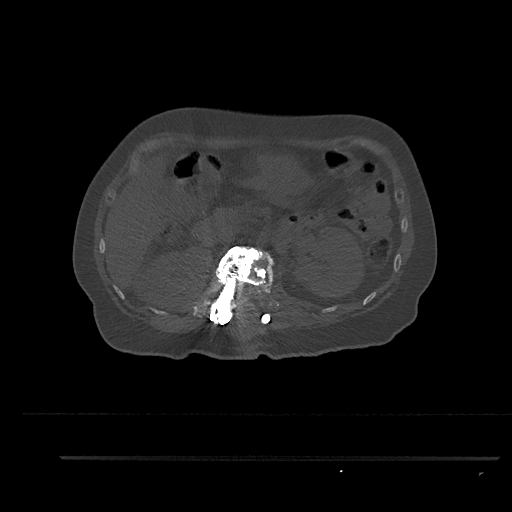
CT including the spine, one axial slice; position 218 of 797 along the scan axis; reconstruction kernel Br40s/3; 120 kVp; bone window (W 1800 / L 400 HU); 0.5 mm slice thickness; 512 × 512 image matrix, field of view 408 × 408 mm. Female patient, age 44 years. Case-level facts recorded for this patient, not image findings: primary cancer: renal; vertebrae with lytic lesions (as recorded): L1.
Structures marked on this image (semi-automatically segmented with operator editing):
- L1 vertebra: box from (x=208, y=246) to (x=276, y=321) px